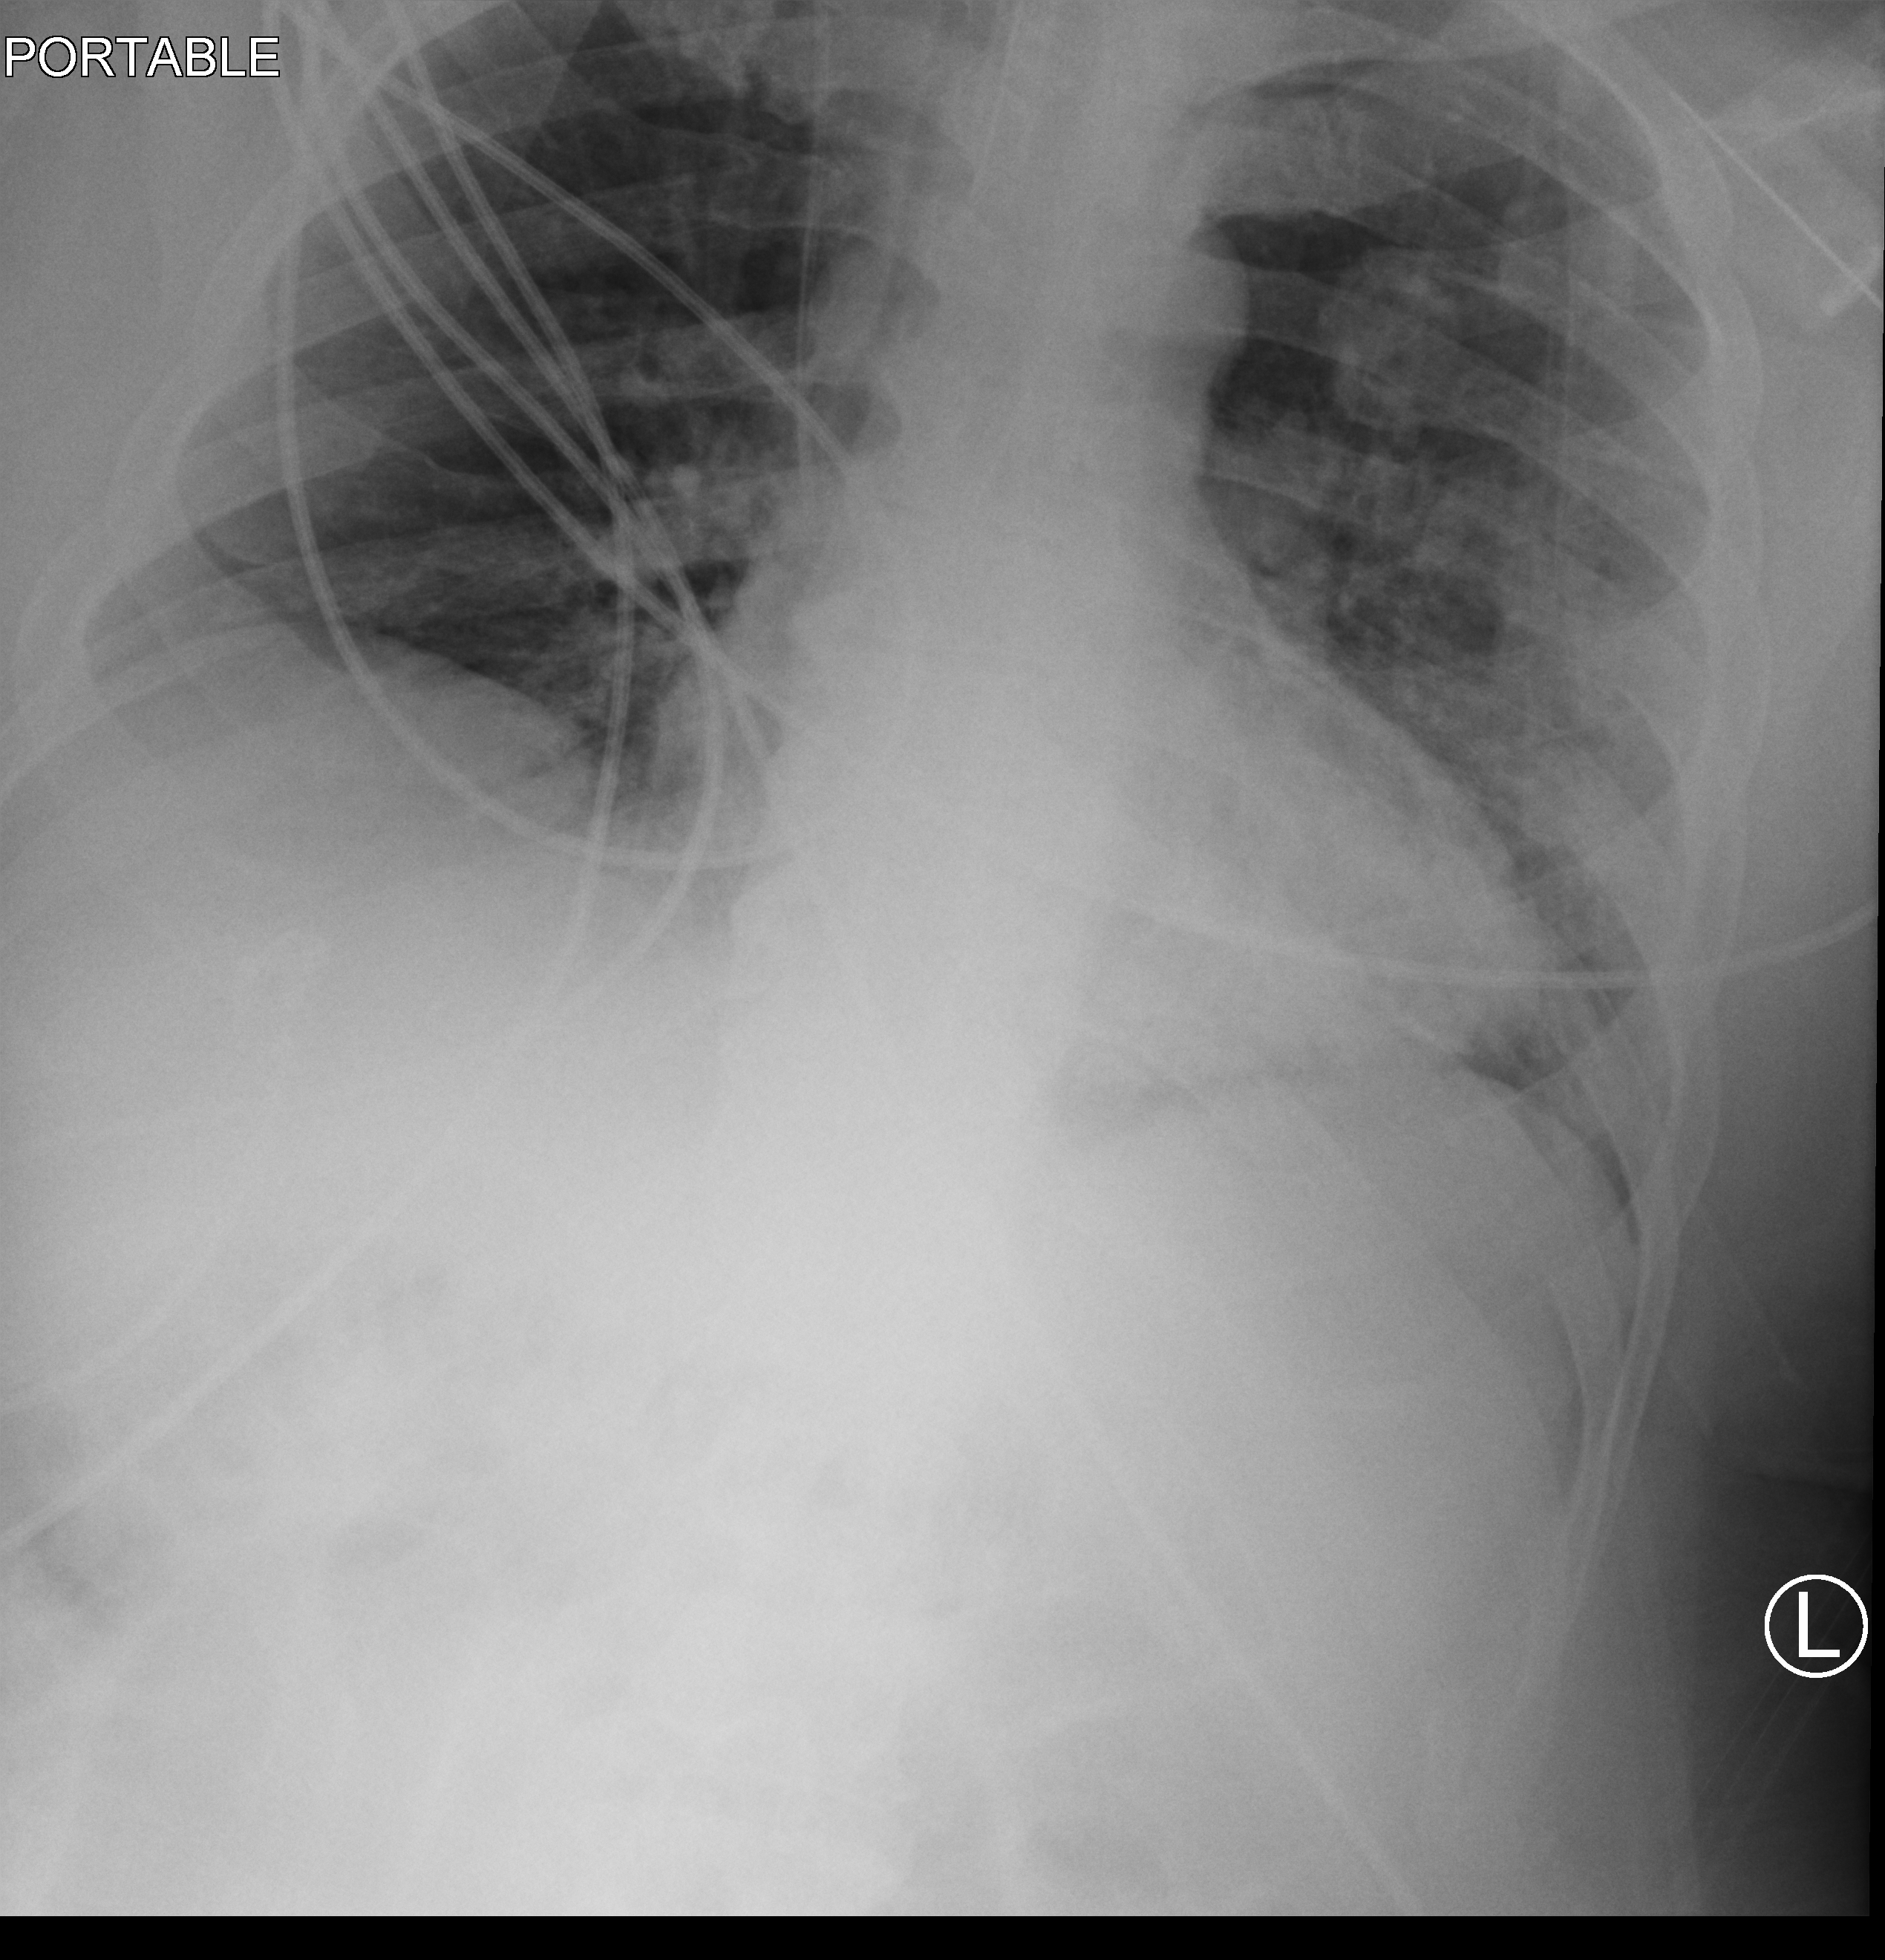
Bedside chest radiograph (computed radiography); anteroposterior (AP) projection. Male patient hospitalised with COVID-19, age 18–59 years.
From the hospital-stay record, not from the radiograph (when in the stay this image was taken is not recorded): diabetes (admission record): no; admitted to intensive care during this hospital stay: yes.